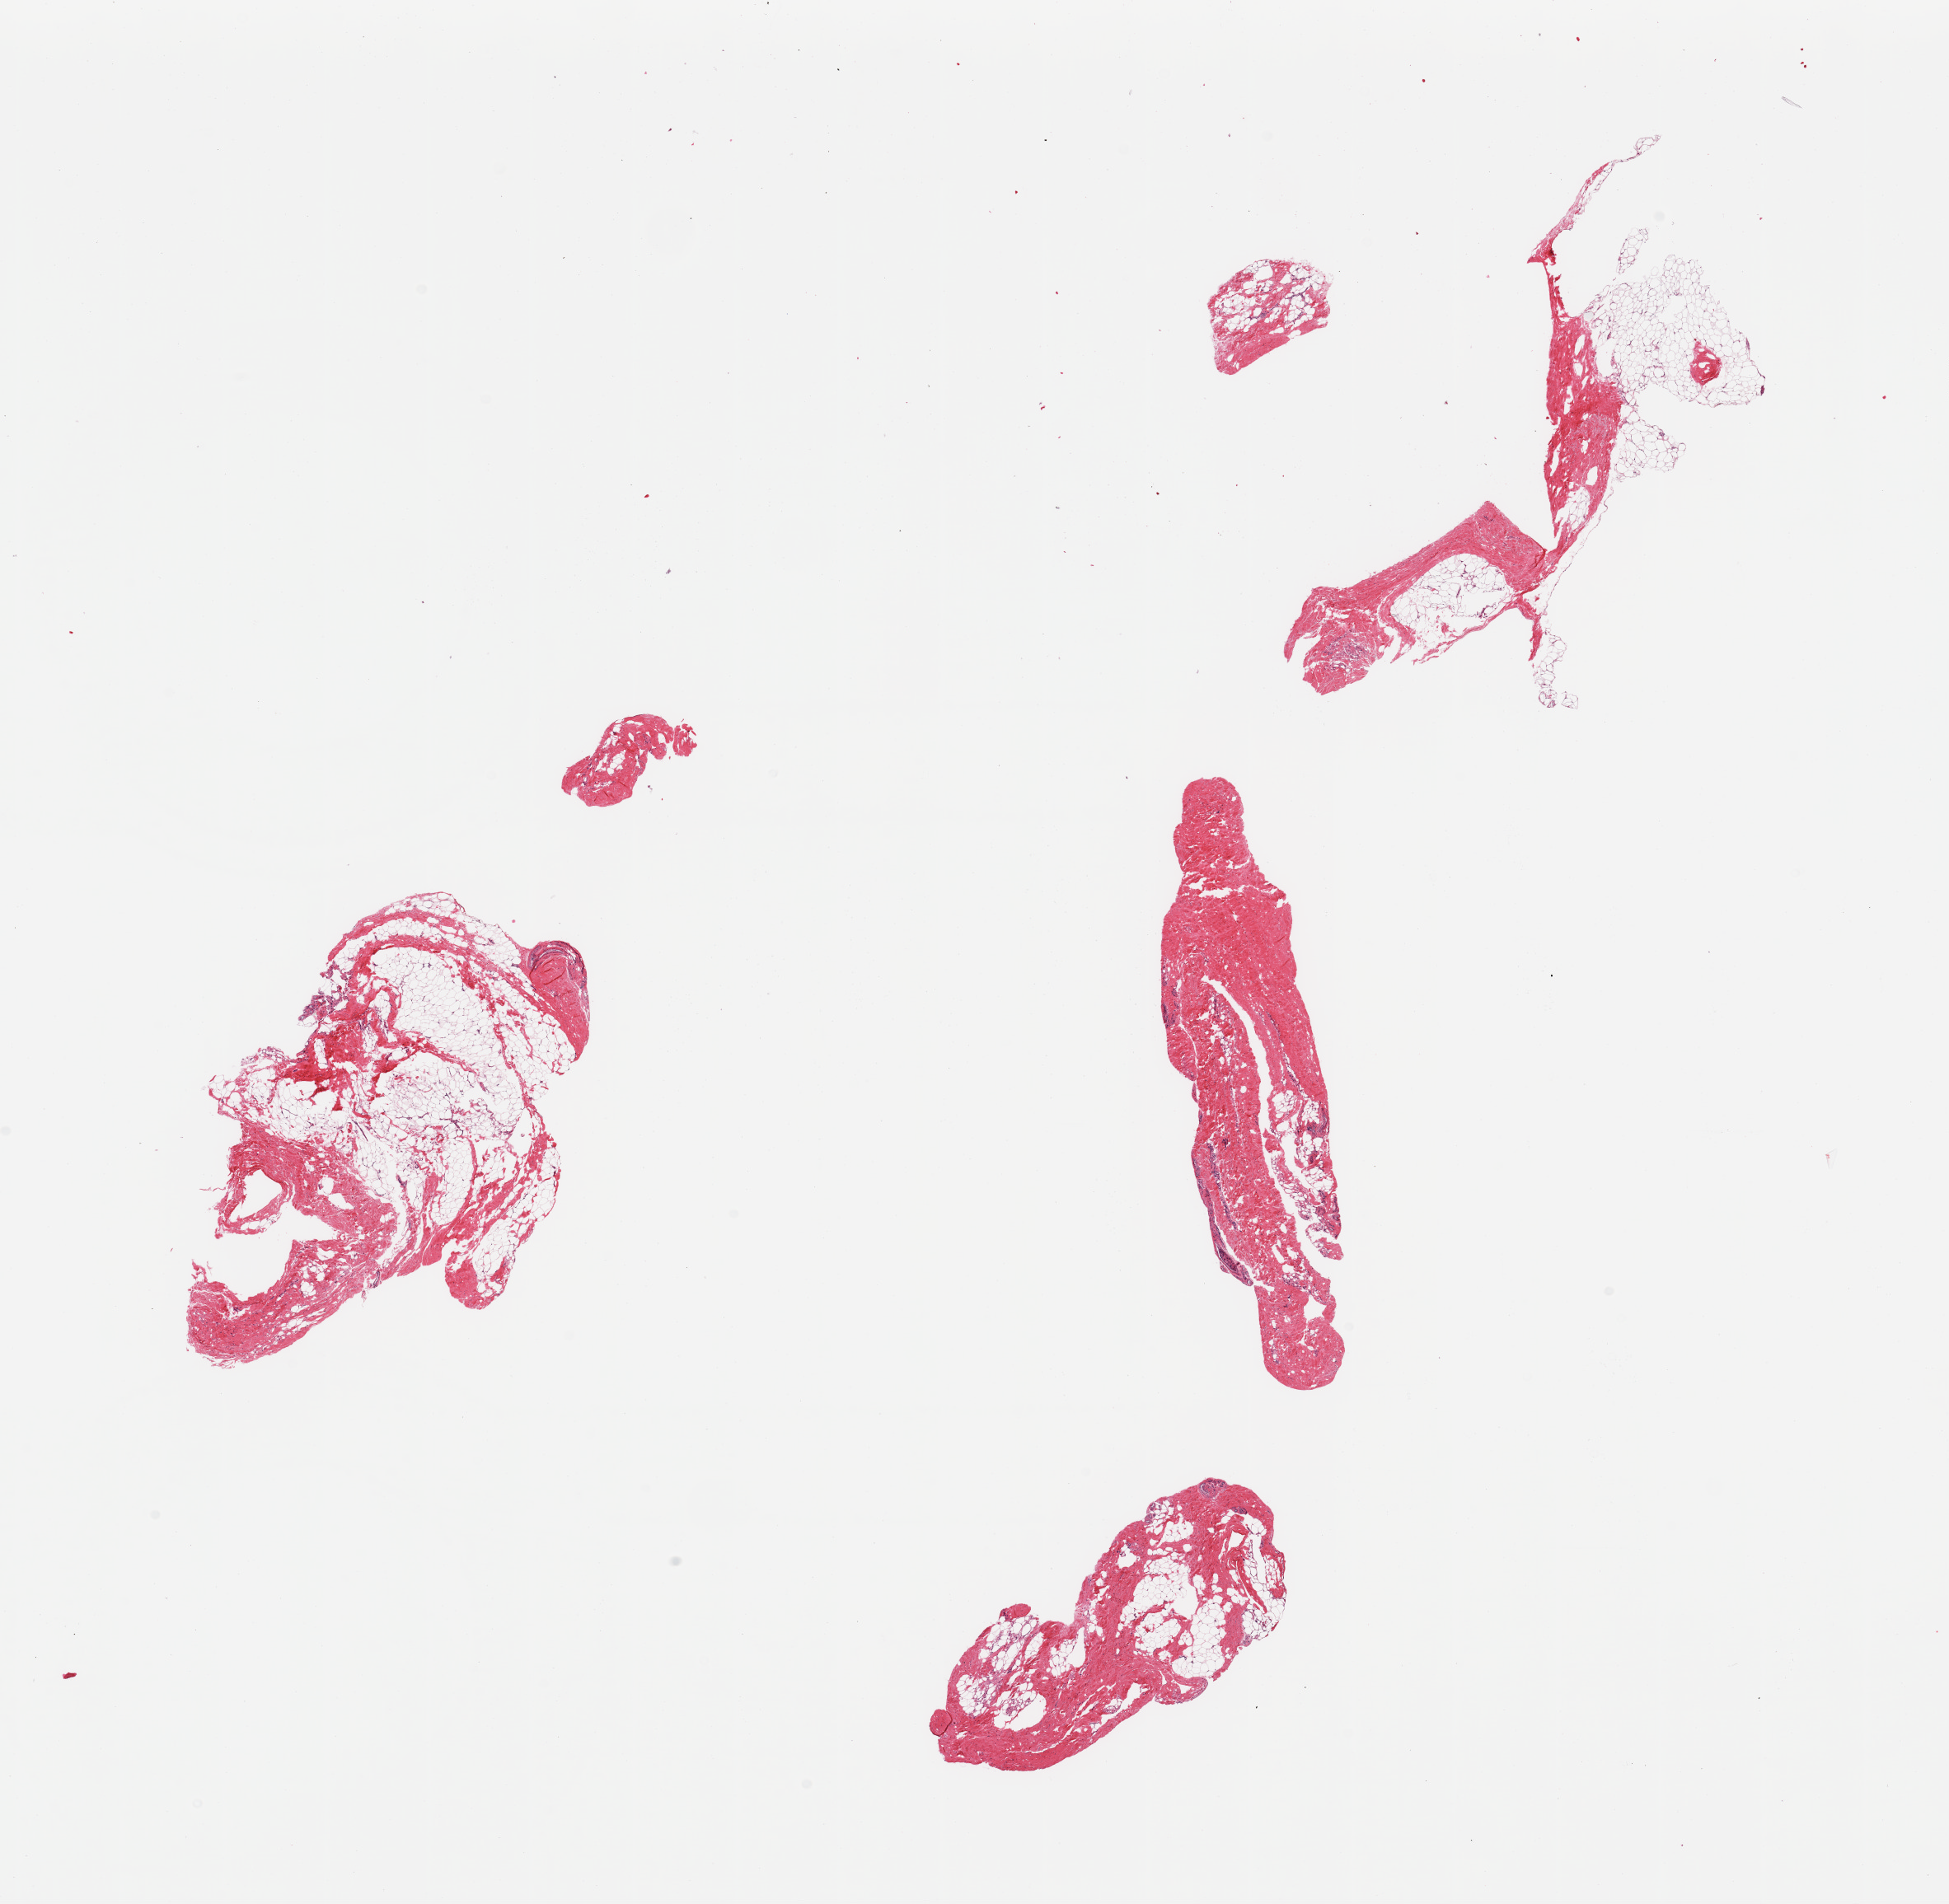
Whole-slide image, H&E stain — a low-resolution overview of the entire scanned area, about 18.7 x 18.3 mm; PAXgene-fixed paraffin-embedded (PFPE) section; sampled site (target tissue): breast; donor tissue sample. Donor sex: male.
• reviewer comment on this tissue sample: 4 pieces (fragmented), fibroadipose elements only